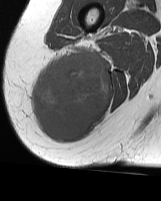
MRI of an extremity soft-tissue mass, one axial slice. Slice 22 of 70 in the series (ordered by position). MR volume resampled by the dataset authors to the PET/CT grid (not the native acquisition matrix). 3.27 mm slice thickness. 161 × 201 image matrix, field of view 157 × 196 mm. Female patient. From the clinical record (not read from this slice): histological type: synovial sarcoma; grade: intermediate; site of the primary tumour: right buttock.
Outlined on this slice (expert contour drawn on MRI and transferred to this co-registered scan by the dataset authors):
- gross tumour volume including surrounding oedema: bounding box [x1, y1, x2, y2] px = [33, 43, 111, 141]
- gross tumour volume (mass): [33, 52, 111, 141]